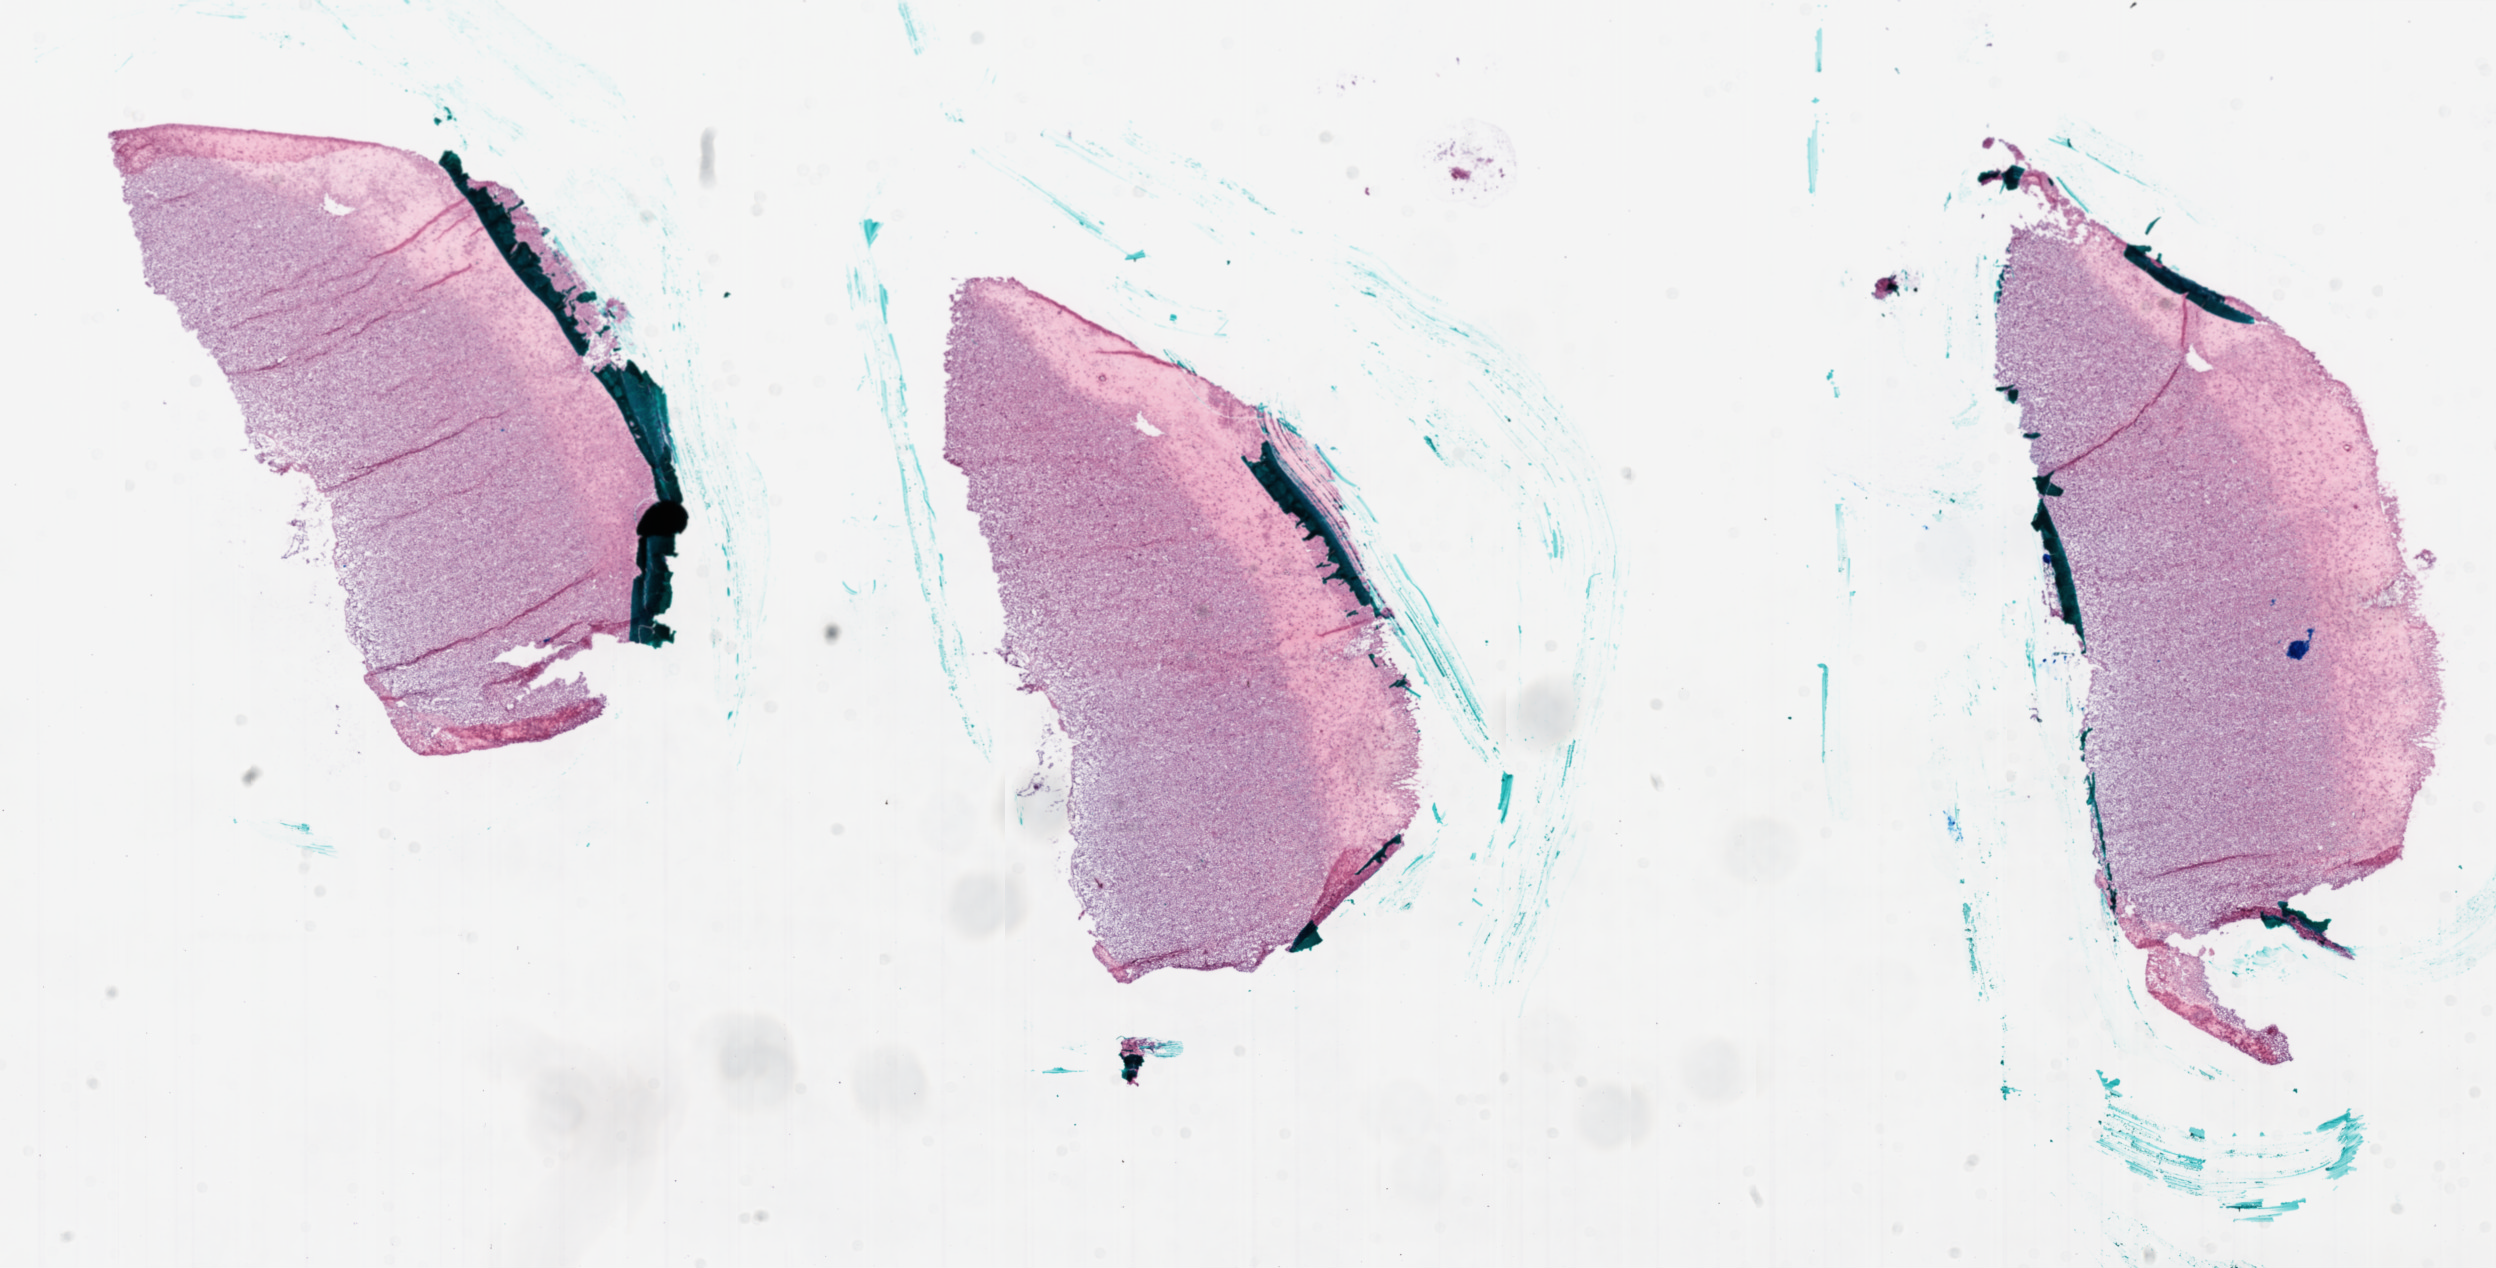
Whole-slide histology image, Hematoxylin and eosin (H&E) stained — shown as a low-resolution overview of the whole scanned area (about 20.0 x 10.1 mm, slide scanned at 20x); frozen section; brain, primary tumour sample. Female patient; age at initial diagnosis 61 years. Pathologist review of this section (percent, as recorded): tumour cells 0%, tumour nuclei 0%, normal cells 100%, stromal cells 0%, necrosis 0%.
Histologic diagnosis: Glioblastoma.